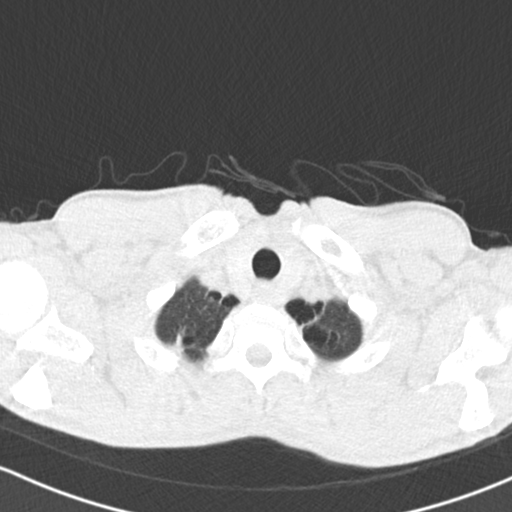
Low-dose screening chest CT, axial slice, baseline annual screen, lung window (W 1500 / L -600 HU), 2 mm slice thickness, standard (soft-tissue) reconstruction kernel (B30f), 120 kVp, slice 20 of 151 in the series, 512 × 512 image matrix, field of view 312 × 312 mm. Male, age 64 years at enrolment.
Expert reader's lesion annotation, box from (x=150, y=319) to (x=203, y=366) px. The exam's reader record, not a measurement of the box and not confirmed to be the same lesion: non-calcified nodule or mass ≥4 mm, right upper lobe, 13 × 11 mm, spiculated (stellate) margins, soft tissue attenuation. Official screen result: positive, change unspecified: nodule(s) >= 4 mm or enlarging nodule(s), mass(es), or other non-specific abnormalities suspicious for lung cancer. Lung cancer was diagnosed 161 days after this screen: adenocarcinoma, NOS, right upper lobe, poorly differentiated (G3), stage IA (AJCC 6th edition), 13 mm at pathology.